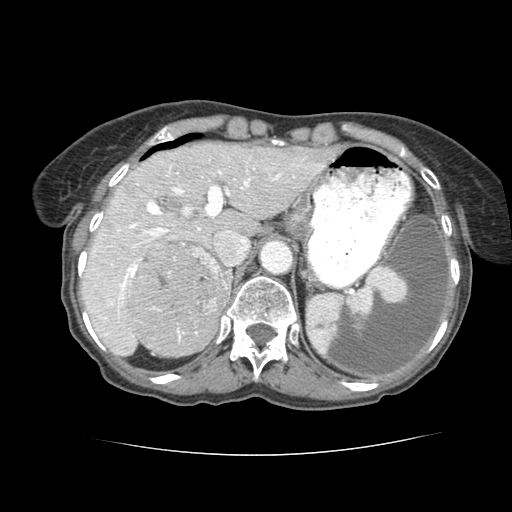
Contrast-enhanced abdominal CT (liver protocol), one axial slice; position 55 of 77 along the scan axis; 120 kVp; soft-tissue window (W 400 / L 40 HU); 2.5 mm slice thickness; 512 × 512 image matrix. From the clinical record (not read from this slice): diagnosis: hepatocellular carcinoma (patient treated with transarterial chemoembolisation; whether this scan precedes or follows treatment is not stated here); TNM stage (as recorded): Stage-I; Child-Pugh class: A; tumour nodularity: uninodular; tumour size: 7.6 cm.
Outlined on this slice (semi-automatically segmented with operator editing):
- liver parenchyma outside the tumour (the mass and vessels are separate outlines, so this box may not span the whole liver): bounding box <78,142,324,354> (left, top, right, bottom; pixels)
- mass: <125,238,228,354>
- liver vessels: <93,159,316,328>